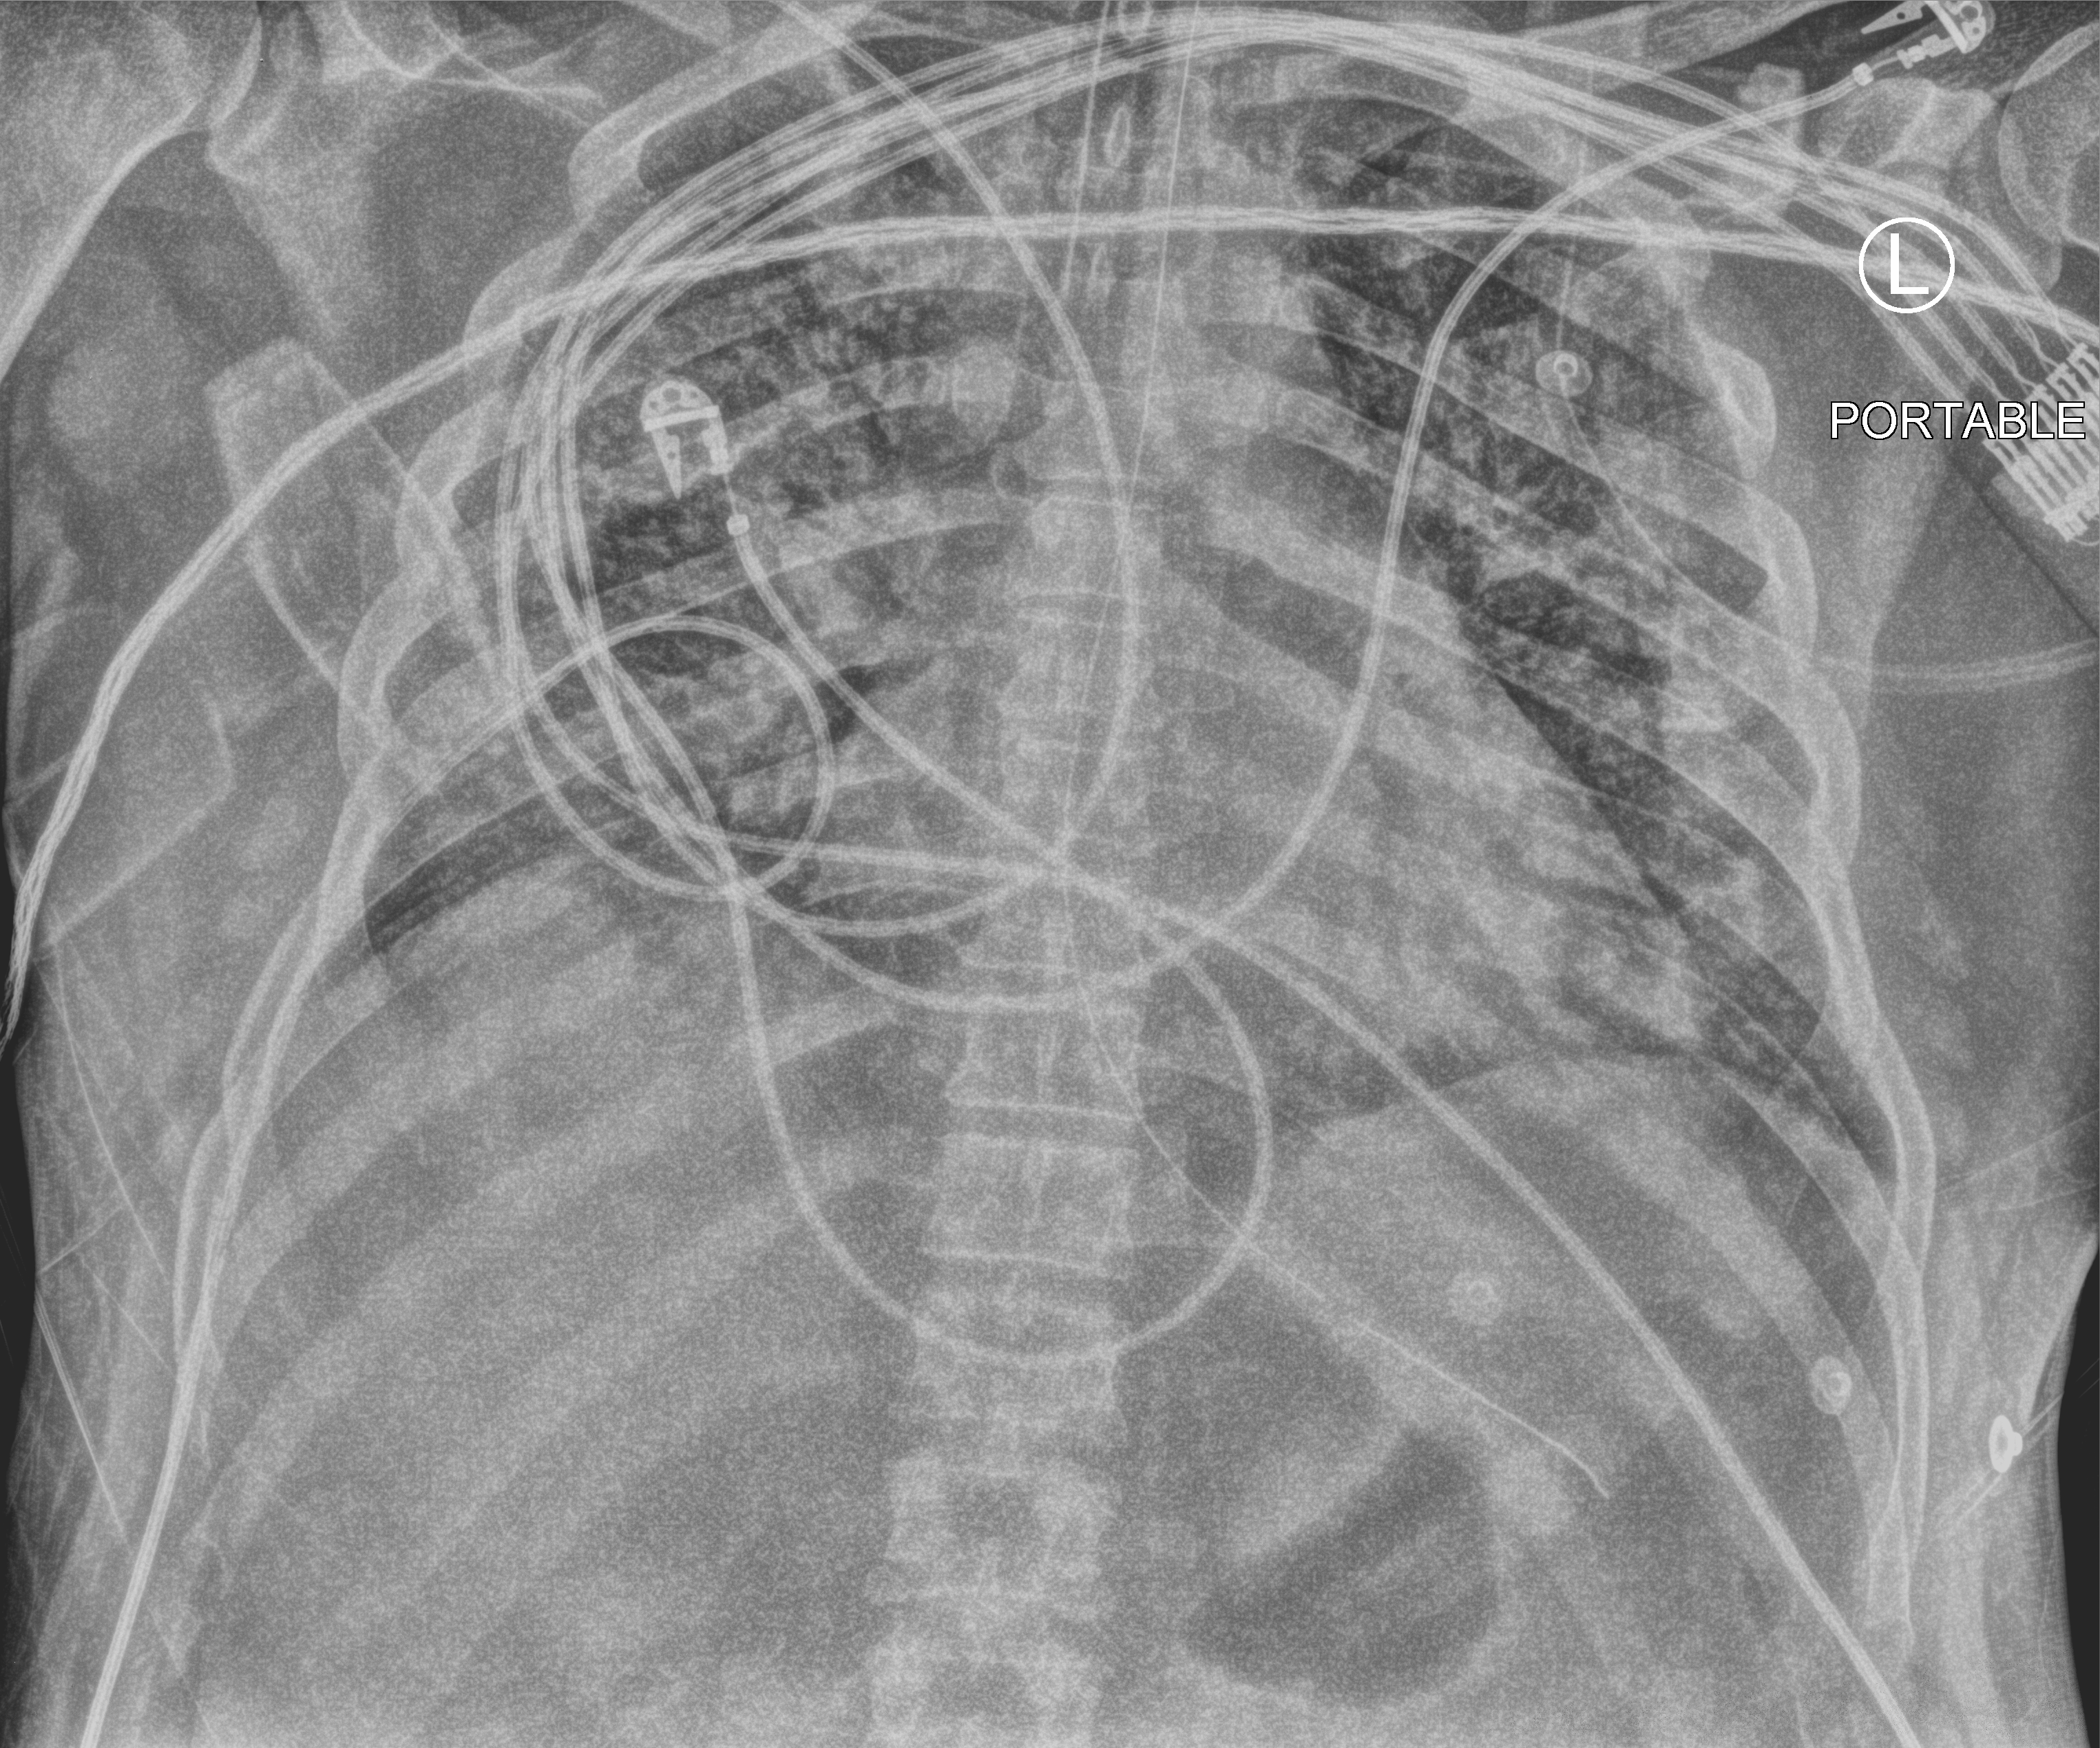
Chest X-ray (portable); anteroposterior (AP) projection. Male patient hospitalised with COVID-19, age 18–59 years.
Admission-level facts for this patient (not findings on this image; timing relative to this image not recorded): length of hospital stay: 26 days.